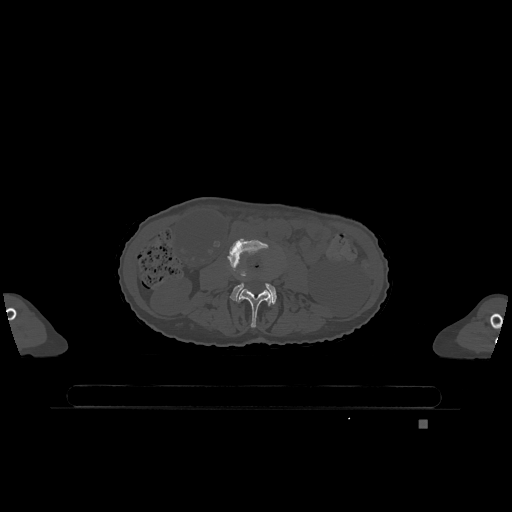
CT including the spine, one axial slice. Slice 335 of 1317 in the series (ordered by position). Bone window (W 1800 / L 400 HU). 0.5 mm slice thickness. 512 × 512 image matrix, field of view 500 × 500 mm. Female patient, age 74 years. From the clinical record (not read from this slice): primary cancer: lung.
Outlined on this slice (semi-automatically segmented with operator editing):
- L3 vertebra: box from (x=238, y=289) to (x=273, y=328) px
- L4 vertebra: (x=229, y=239)–(x=277, y=304)